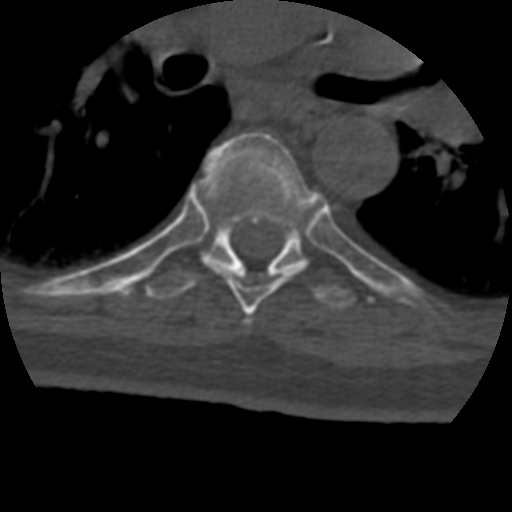
CT including the spine, one axial slice; slice 292 of 399 in the series (ordered by position); bone window (W 1800 / L 400 HU); 1.25 mm slice thickness; 512 × 512 image matrix, field of view 160 × 160 mm. Patient age 69 years. From the clinical record (not read from this slice): primary cancer: prostate.
Outlined on this slice (semi-automatic segmentation, software-assisted and operator-edited):
- T5 vertebra: bounding box (x1, y1, x2, y2) in pixels: (247, 321, 250, 323)
- T6 vertebra: (202, 131, 317, 315)
- T7 vertebra: (145, 214, 357, 309)